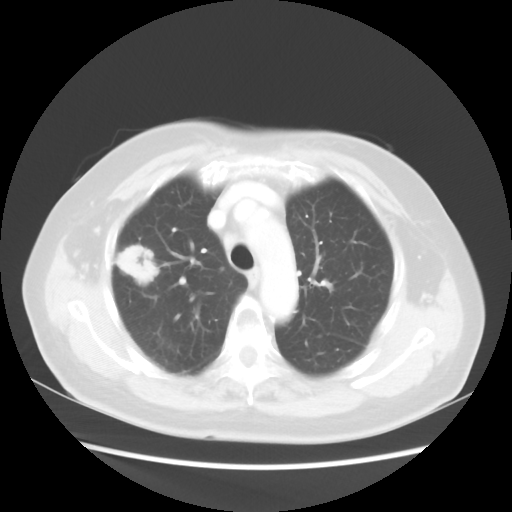
Chest CT, one axial slice; position 35 of 48 along the scan axis; reconstruction kernel STANDARD; lung window (W 1500 / L -600 HU); 5 mm slice thickness; 512 × 512 image matrix. Female patient, age 75 years. Case-level facts recorded for this patient, not image findings: clinical TNM (as recorded): T1c N0 M0.
Structures marked on this image (bounding box drawn by a radiologist):
- lung tumour (recorded histology: adenocarcinoma): bounding box <113,244,161,286> (left, top, right, bottom; pixels)